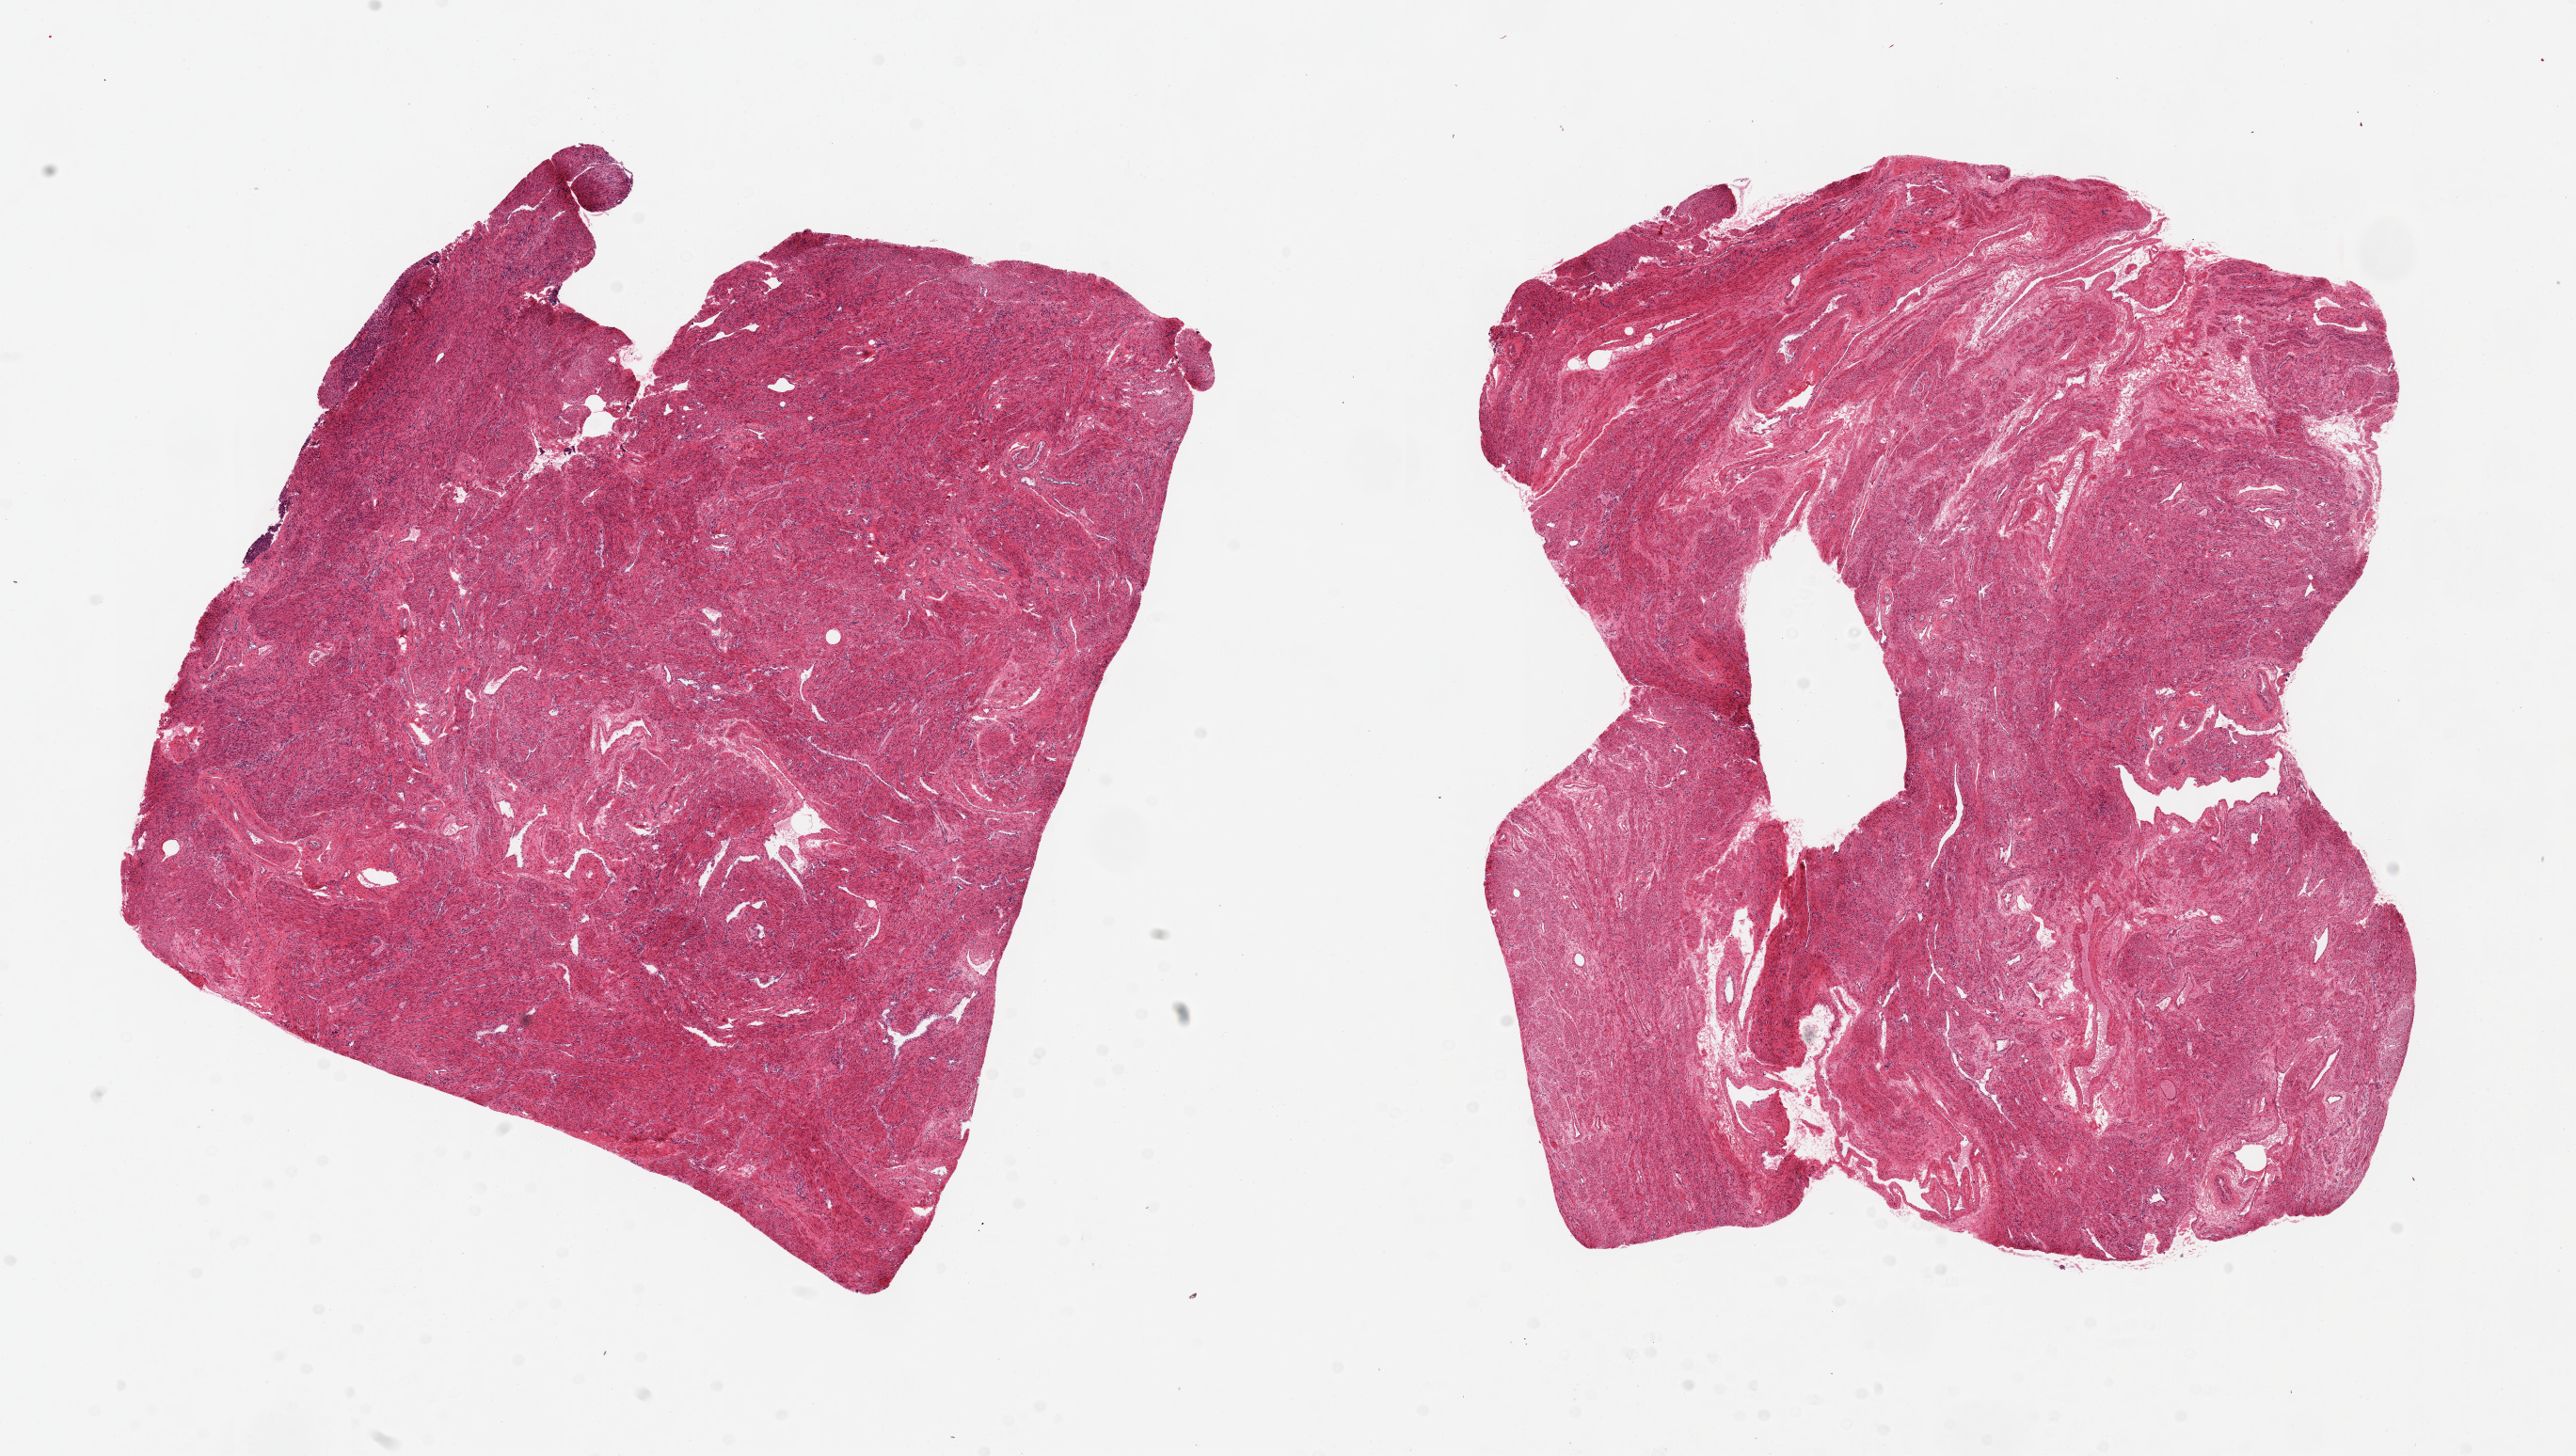
Digitized hematoxylin and eosin (H&E)-stained section, brightfield — whole scanned area (about 21.7 x 12.2 mm) shown as a low-resolution overview; PAXgene-fixed, paraffin-embedded tissue; sampled site (target tissue): uterus; tissue donor sample. Donor: female.
Pathologist's review note for this sample: 2 pieces ~9x8mm all muscularis, no viable endometrium noted.